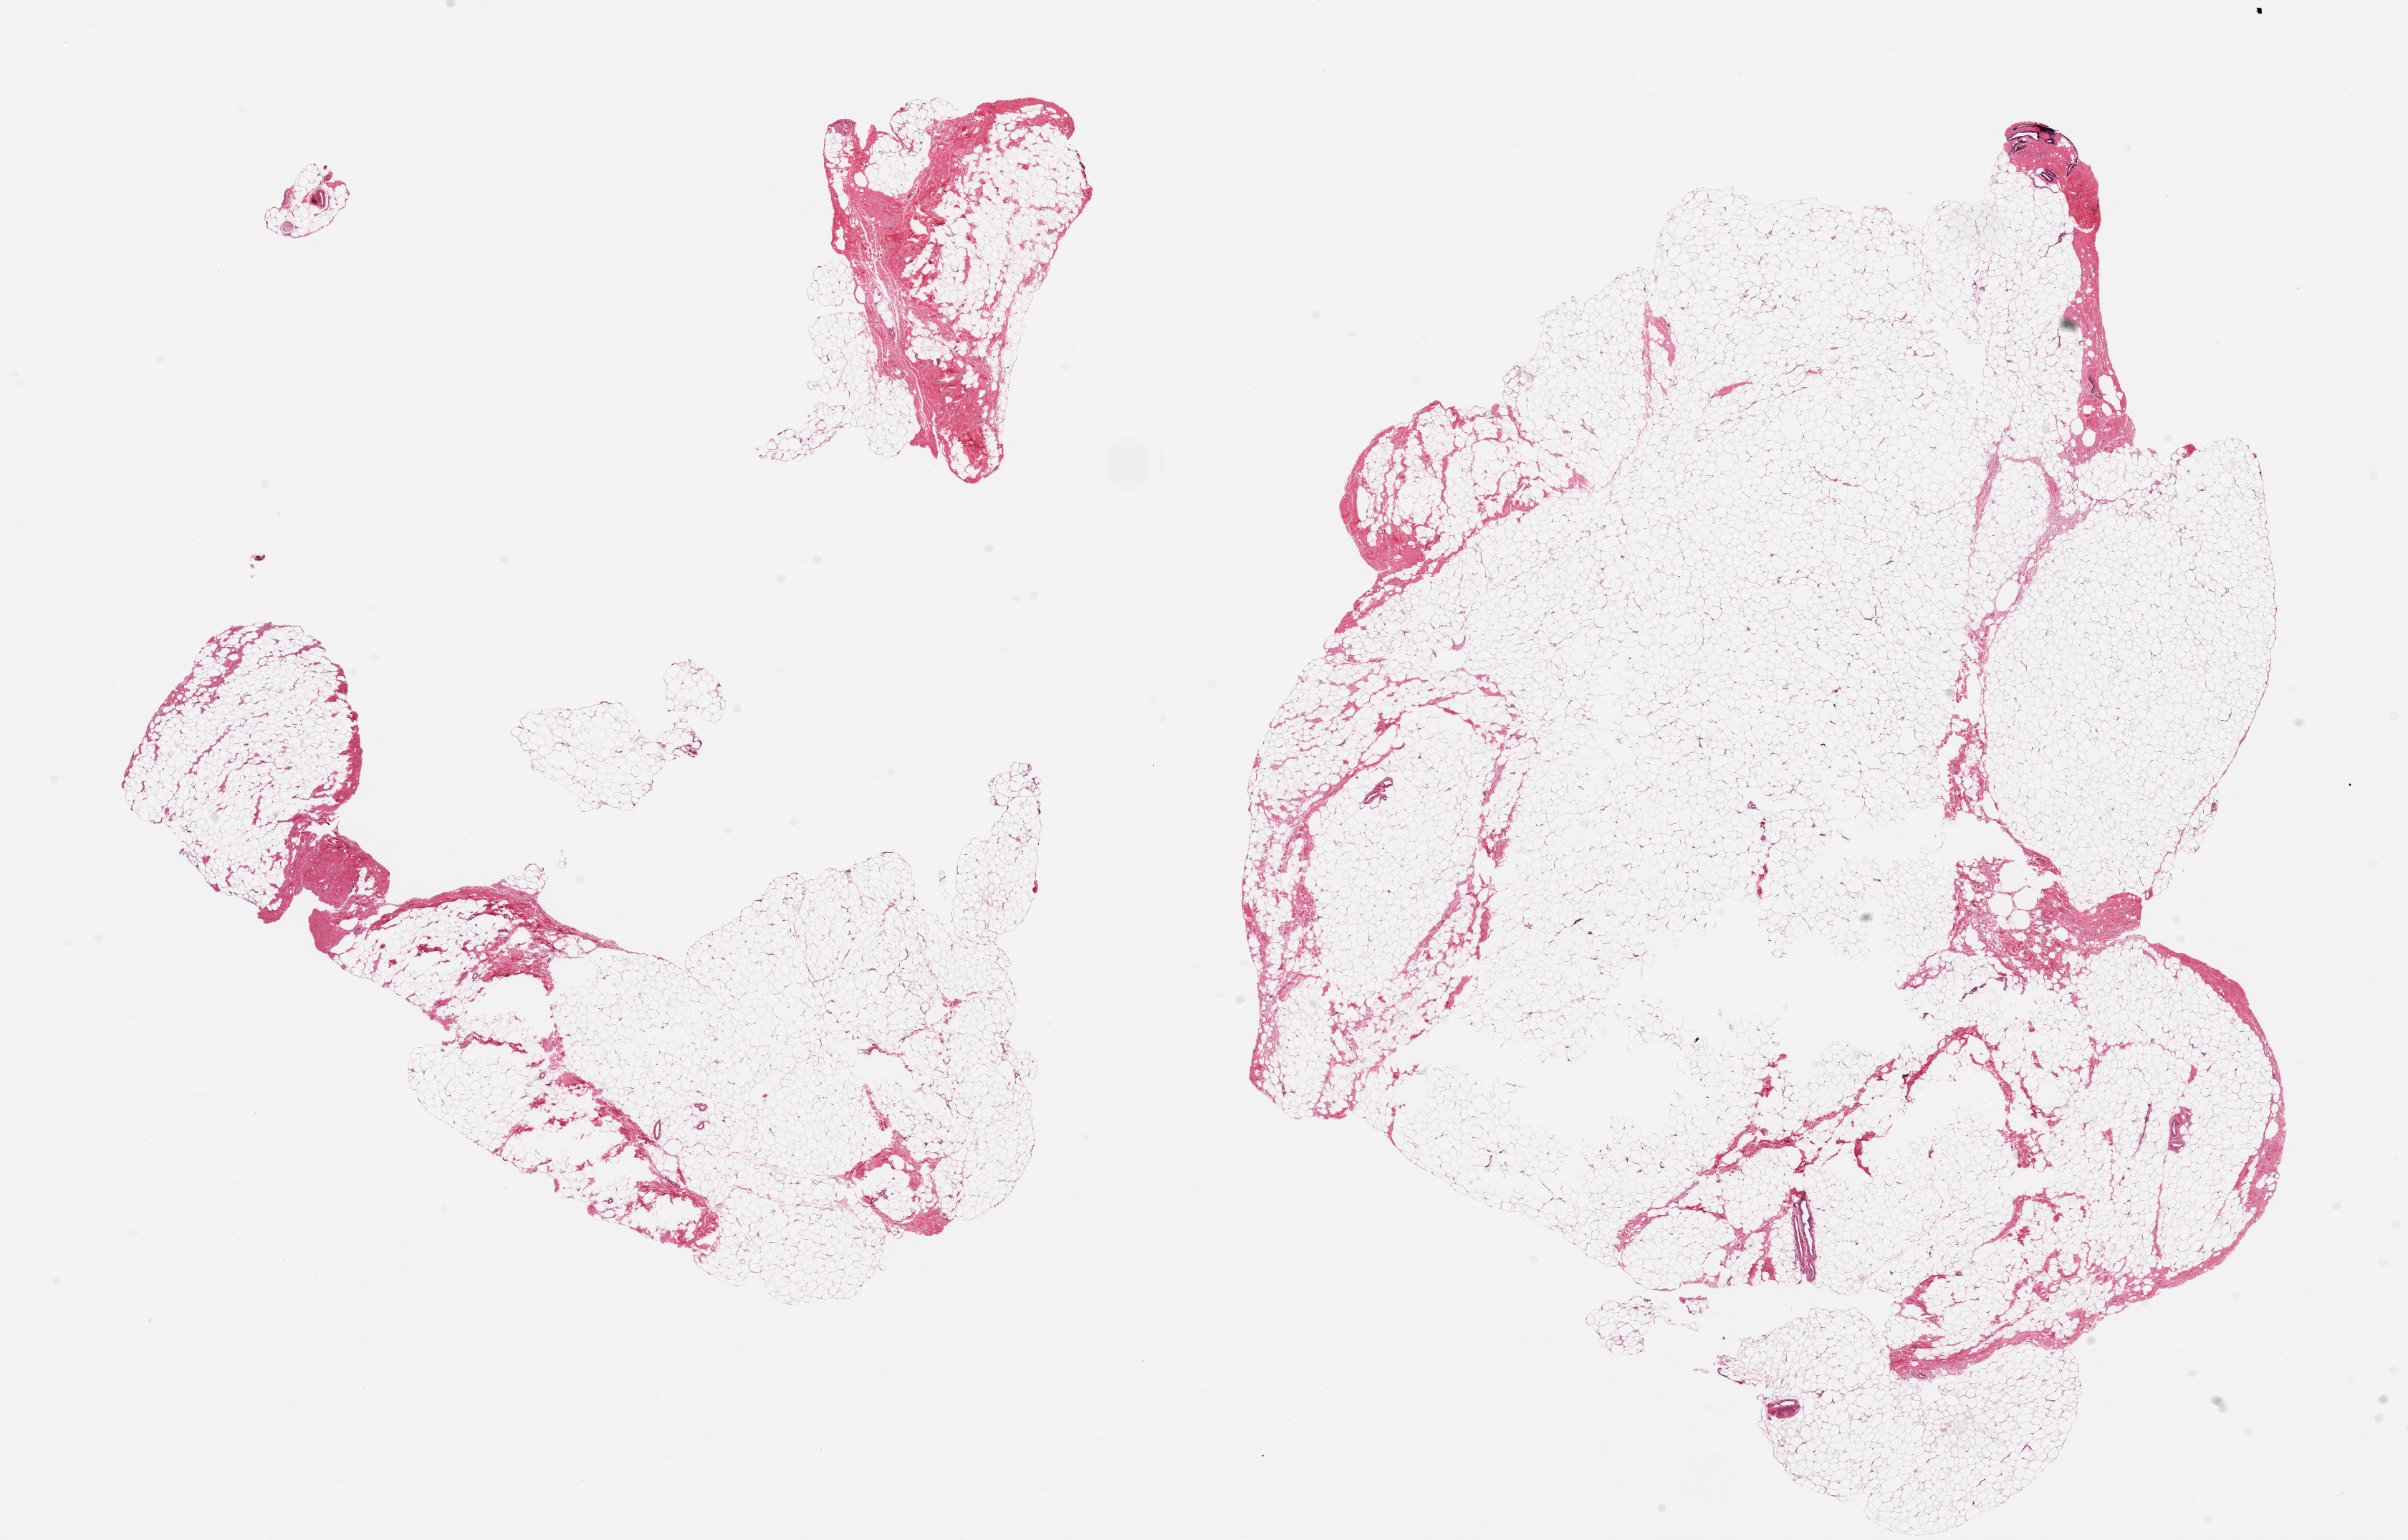
Whole-slide image, H&E stain, whole scanned area (about 26.6 x 17.0 mm) shown as a low-resolution overview; PAXgene-fixed paraffin-embedded (PFPE) section; sampled site (target tissue): breast; tissue donor sample.
- review note (as recorded): 2 aliquots, ~12x10mm. Minute focus of ductal elements; >99% adipose tissue